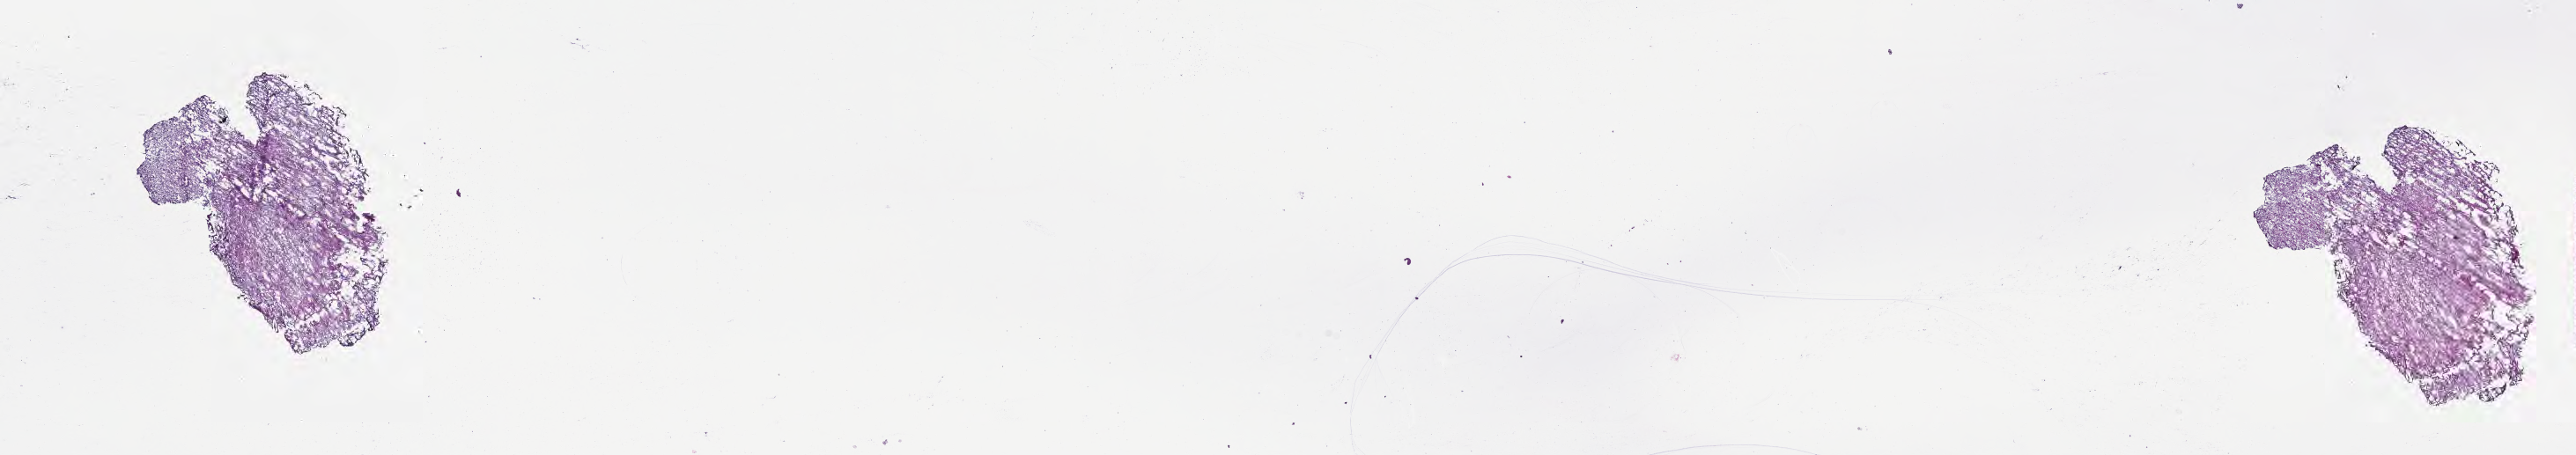
Whole-slide image, H&E stain of tumor tissue from the brain, a low-resolution overview of the entire scanned area, about 23.6 x 4.2 mm. Cryosection (OCT / tissue freezing medium). Patient: male, age 111 months (9 years 3 months).
Diagnosis (ICD-O-3 morphology term): Pilocytic astrocytoma.